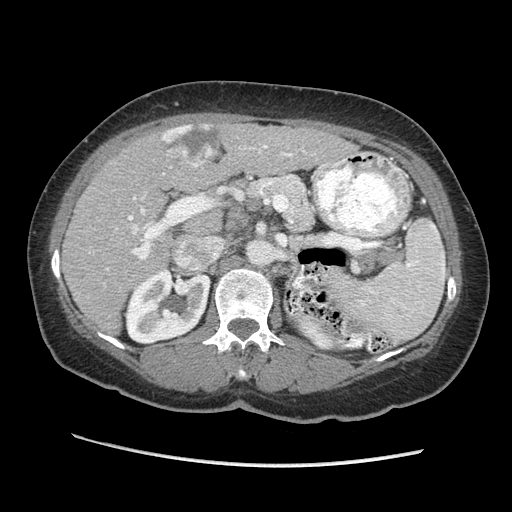
Contrast-enhanced abdominal CT (liver protocol), one axial slice; slice 125 of 170 in the series (ordered by position); reconstruction kernel STANDARD; soft-tissue window (W 400 / L 40 HU); 2.5 mm slice thickness; 512 × 512 image matrix, field of view 360 × 360 mm. From the clinical record (not read from this slice): diagnosis: hepatocellular carcinoma (patient treated with transarterial chemoembolisation; whether this scan precedes or follows treatment is not stated here); TNM stage (as recorded): Stage-II; Child-Pugh class: A; tumour differentiation: no biopsy; tumour size: 4 cm.
Structures marked on this image (semi-automatic segmentation, software-assisted and operator-edited):
- liver parenchyma outside the tumour (the mass and vessels are separate outlines, so this box may not span the whole liver): bounding box (x1, y1, x2, y2) in pixels: (62, 122, 356, 332)
- mass: (159, 123, 221, 168)
- liver vessels: (128, 145, 346, 260)